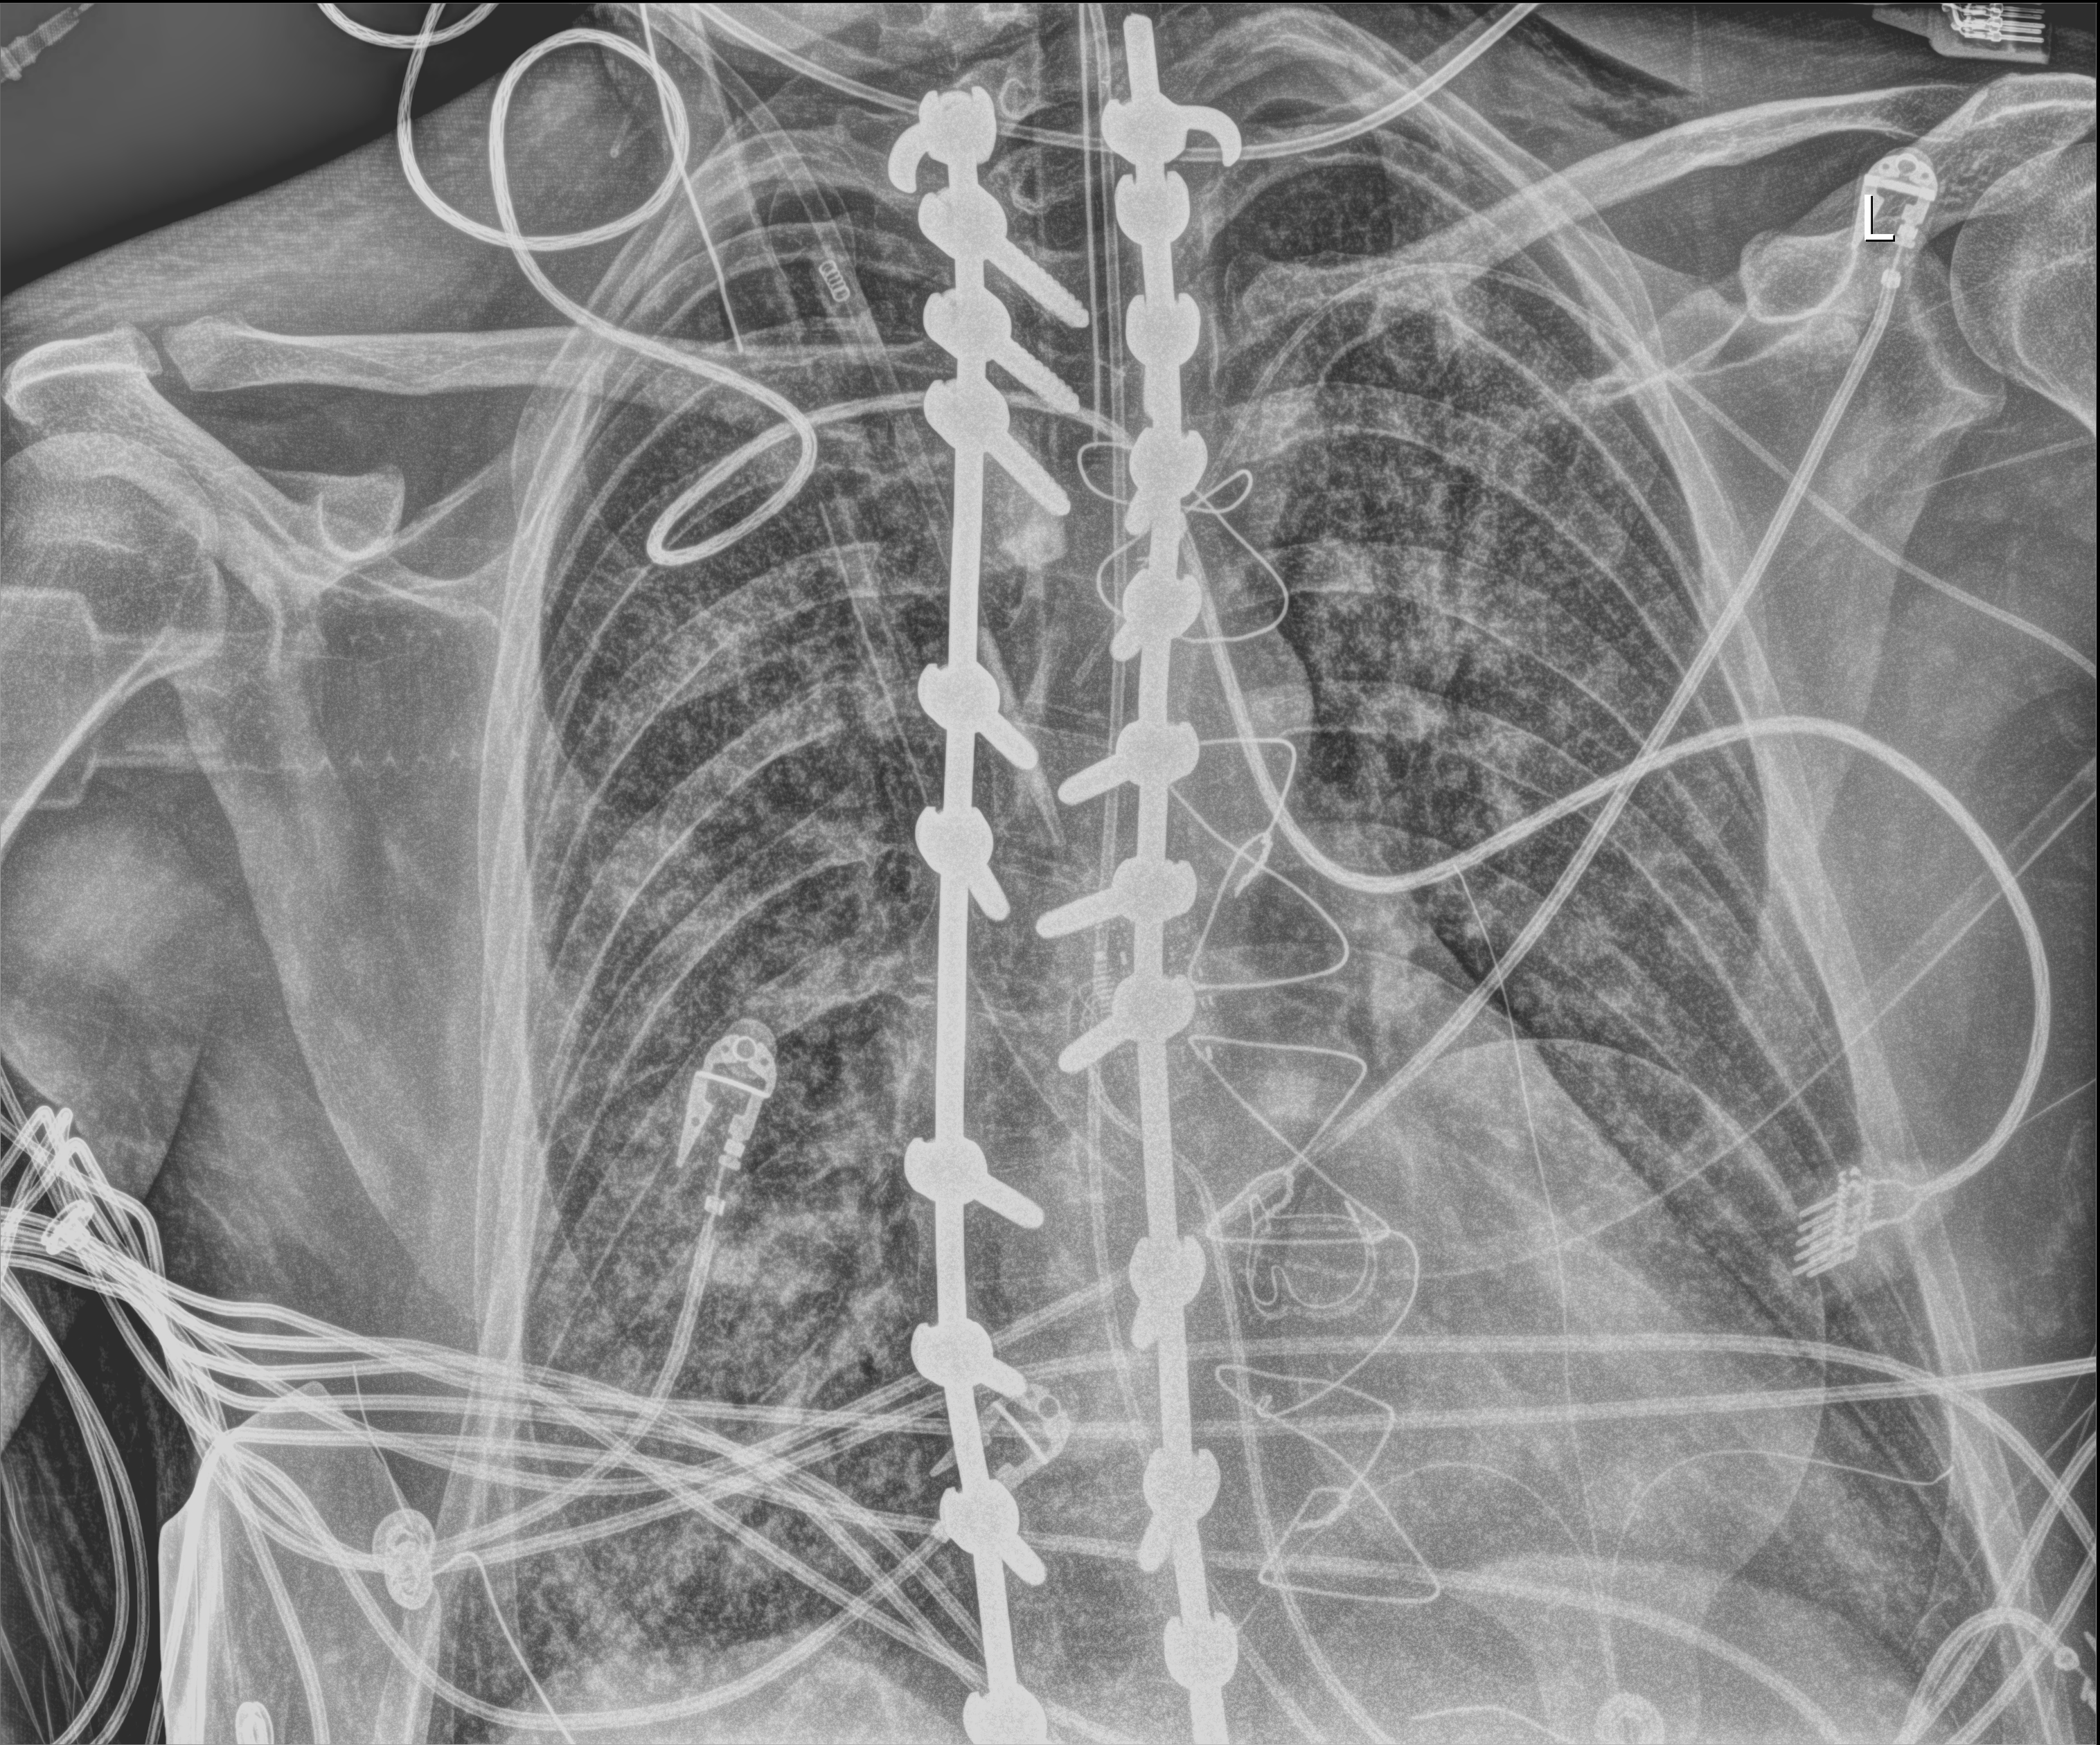
Chest X-ray (portable), anteroposterior (AP) projection. Adult patient hospitalised with COVID-19, age 18–59 years.
From the hospital-stay record, not from the radiograph (when in the stay this image was taken is not recorded):
- chronic kidney disease (admission record): no
- mechanically ventilated during this hospital stay: yes
- admitted to intensive care during this hospital stay: yes